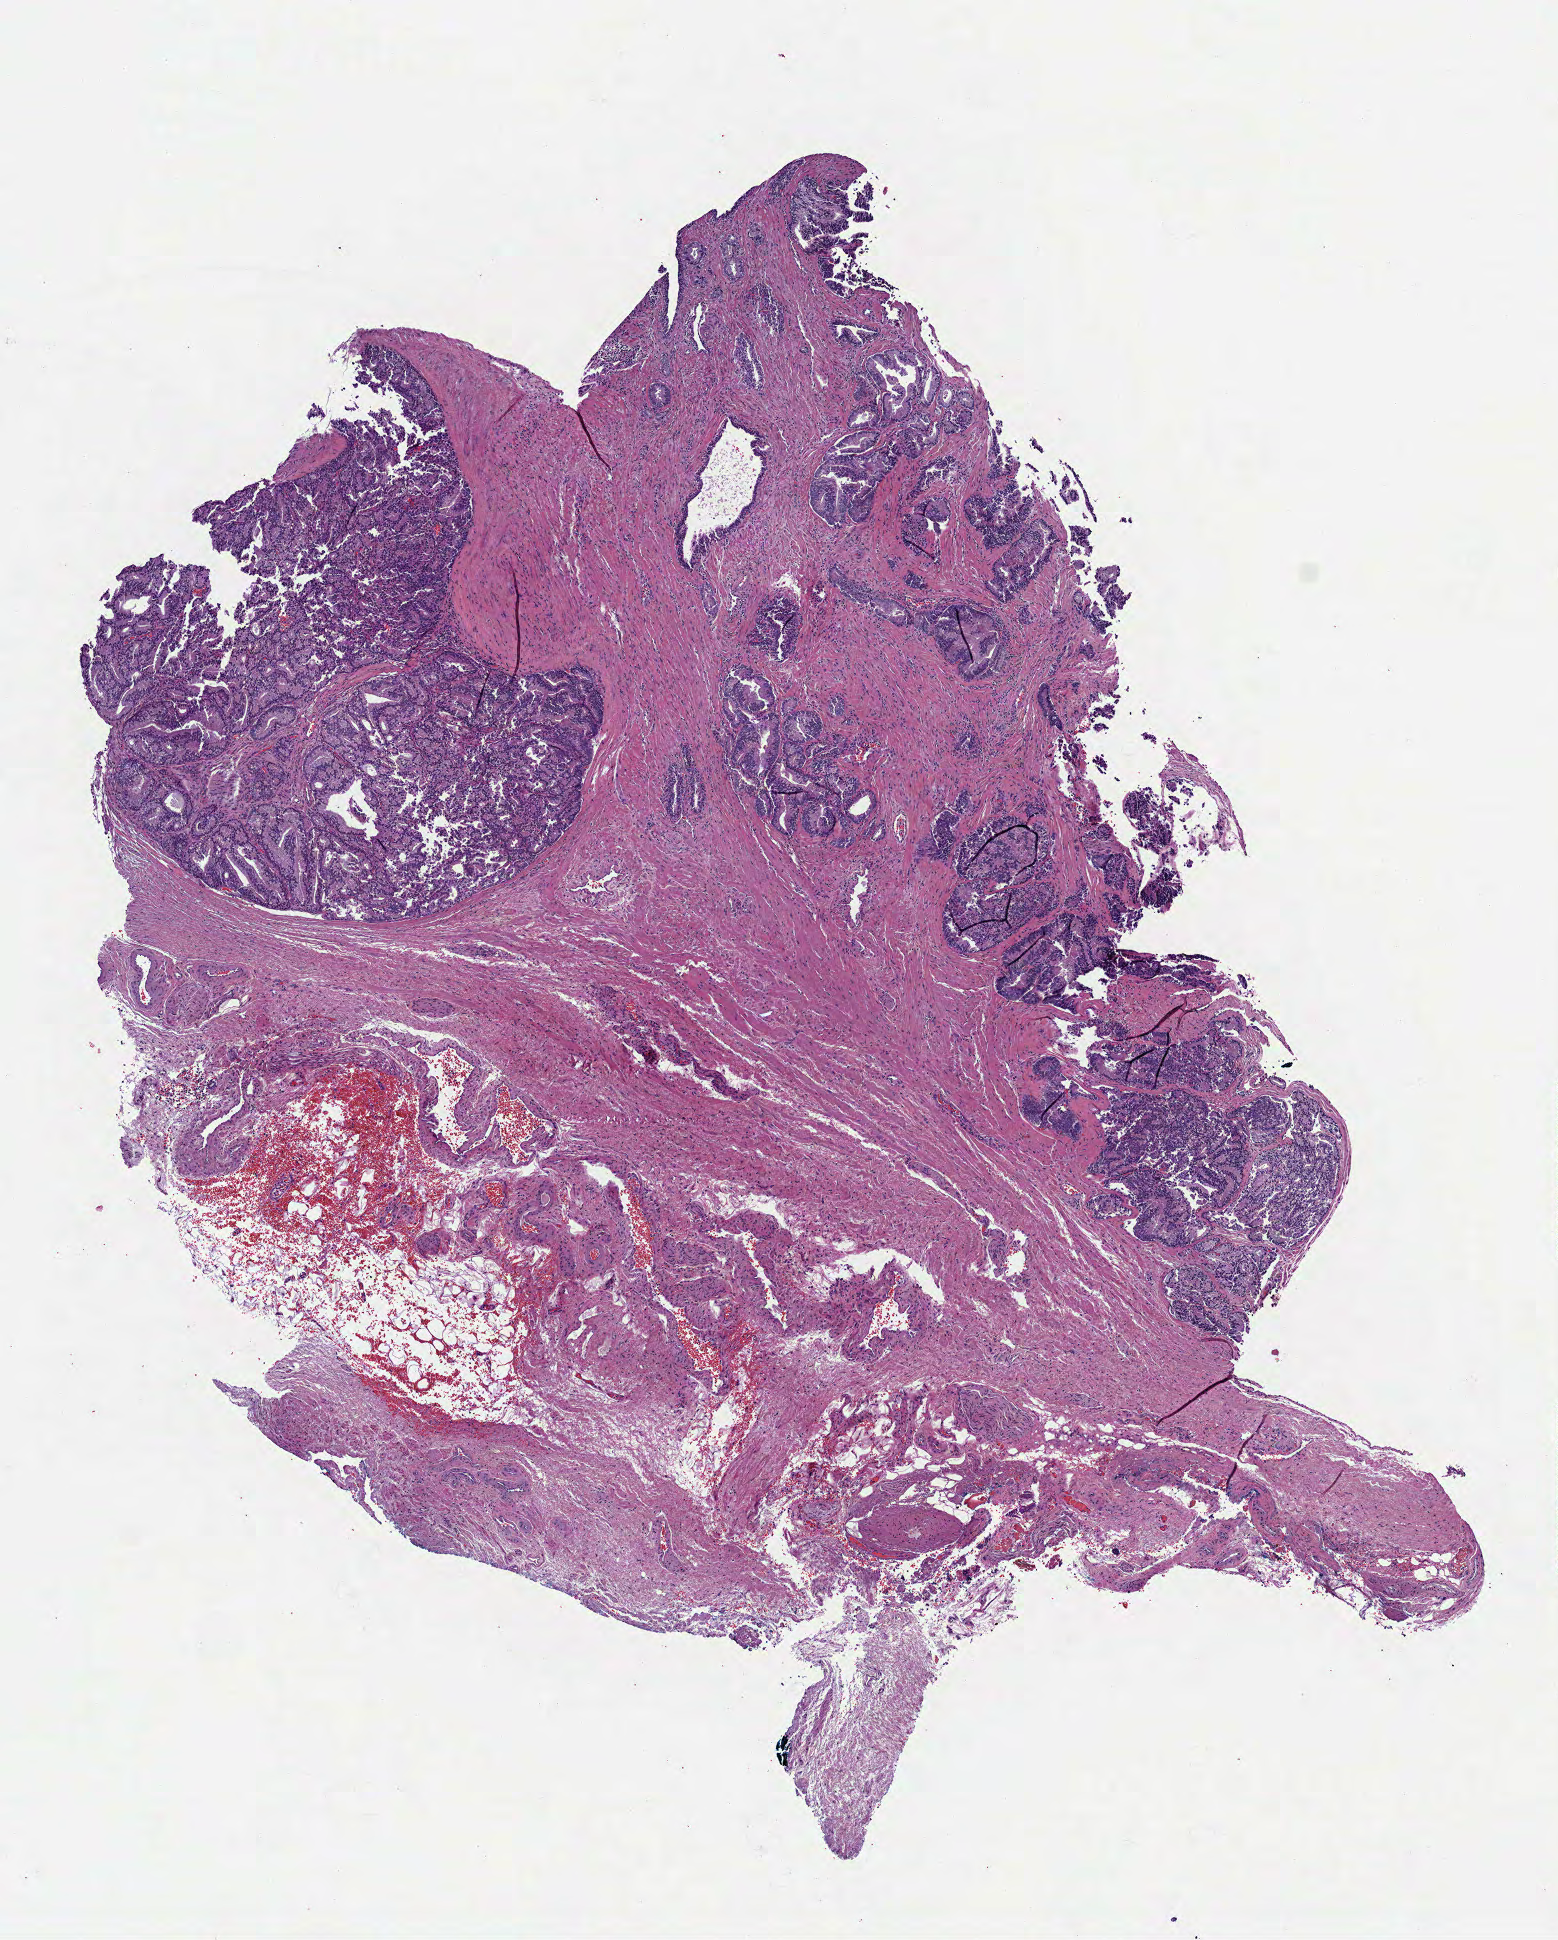
Digitized H&E tissue section (whole slide), a low-resolution overview of the entire scanned area, about 6.3 x 7.8 mm (acquisition: 40x scan); FFPE section; sample: primary tumour, prostate. Male, age 52 years at initial diagnosis.
Diagnosis: Adenocarcinoma, NOS.